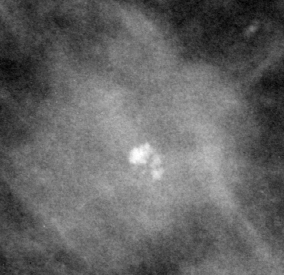
Cropped region of a digitized screen-film mammogram centred on a radiologist-marked abnormality; left breast; MLO view; BI-RADS breast density category 3 (scale 1–4).
Marked abnormality: mass, shape irregular, margins ill defined / spiculated; BI-RADS assessment category 4; pathology result (as recorded, not read from the image): malignant.